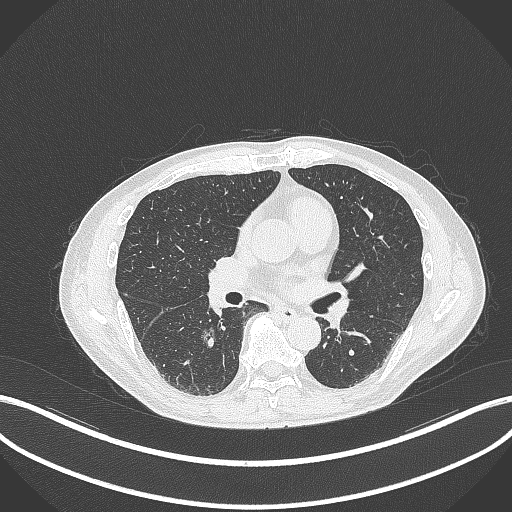
Chest CT, one axial slice. Position 167 of 323 along the scan axis. 120 kVp. Lung window (W 1500 / L -600 HU). 1 mm slice thickness. 512 × 512 image matrix. Male patient, age 61 years. Case-level facts recorded for this patient, not image findings: clinical TNM (as recorded): T1c N0 M0.
Outlined on this slice (bounding box drawn by a radiologist):
- lung tumour (recorded histology: adenocarcinoma): bounding box <198,323,221,344> (left, top, right, bottom; pixels)